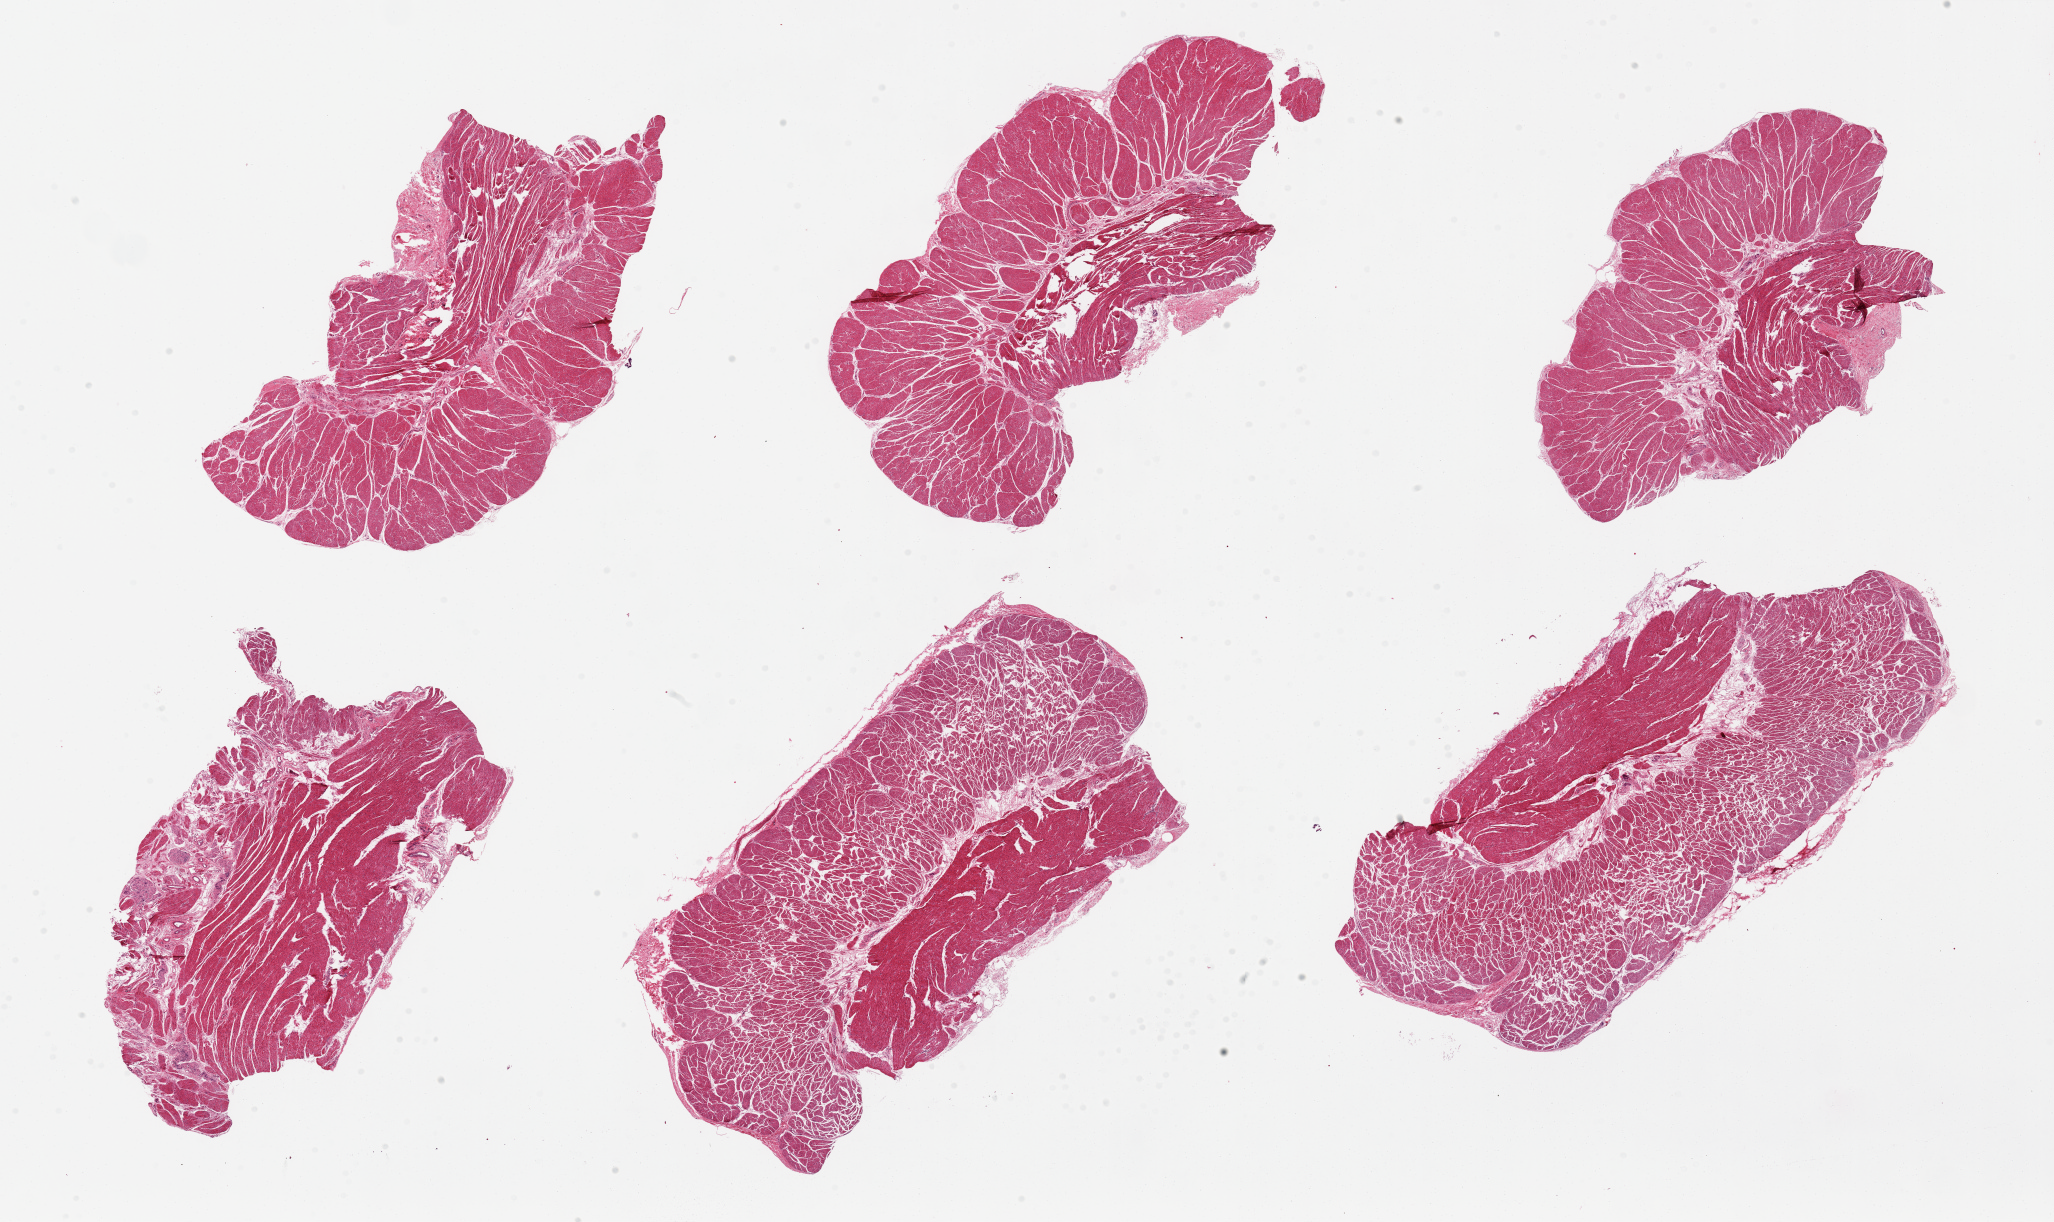
Digitized H&E-stained section, brightfield, whole scanned area (about 32.5 x 19.3 mm, acquisition: 20x scan) shown as a low-resolution overview; PAXgene-fixed, paraffin-embedded tissue; section of esophageal muscle (target tissue); donor tissue sample. Donor sex: female.
Review note (as recorded): 6 pieces. up to 10x5mm; Well trimmed.